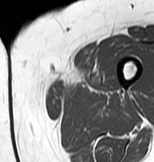
MRI of an extremity soft-tissue mass, one axial slice; slice 2 of 83 in the series (ordered by position); MR volume resampled by the dataset authors to the PET/CT grid (not the native acquisition matrix); 3.27 mm slice thickness; 154 × 162 image matrix, field of view 150 × 158 mm. Female patient. From the clinical record (not read from this slice): histological type: myxofibrosarcoma; grade: intermediate; site of the primary tumour: left thigh.
Outlined on this slice (expert contour drawn on MRI and transferred to this co-registered scan by the dataset authors):
- gross tumour volume including surrounding oedema: bounding box [x1, y1, x2, y2] px = [53, 71, 107, 96]